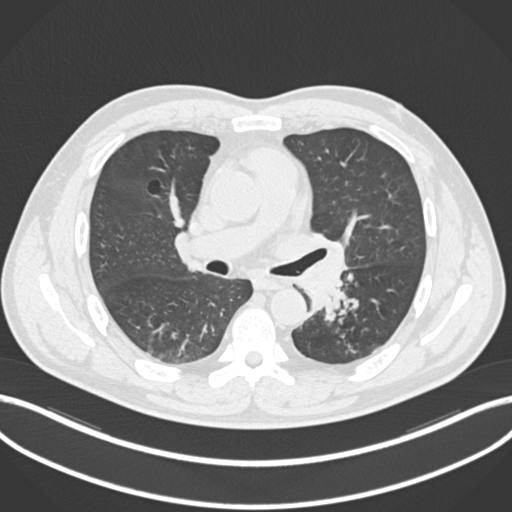
Chest CT, one axial slice; slice 130 of 223 in the series (ordered by position); 120 kVp; lung window (W 1500 / L -600 HU); 512 × 512 image matrix, field of view 400 × 400 mm. Patient: male, 50 years. Case-level facts recorded for this patient, not image findings: clinical TNM (as recorded): T2a N3 M0.
Structures marked on this image (bounding box drawn by a radiologist):
- lung tumour (recorded histology: squamous cell carcinoma): box from (x=295, y=244) to (x=360, y=325) px